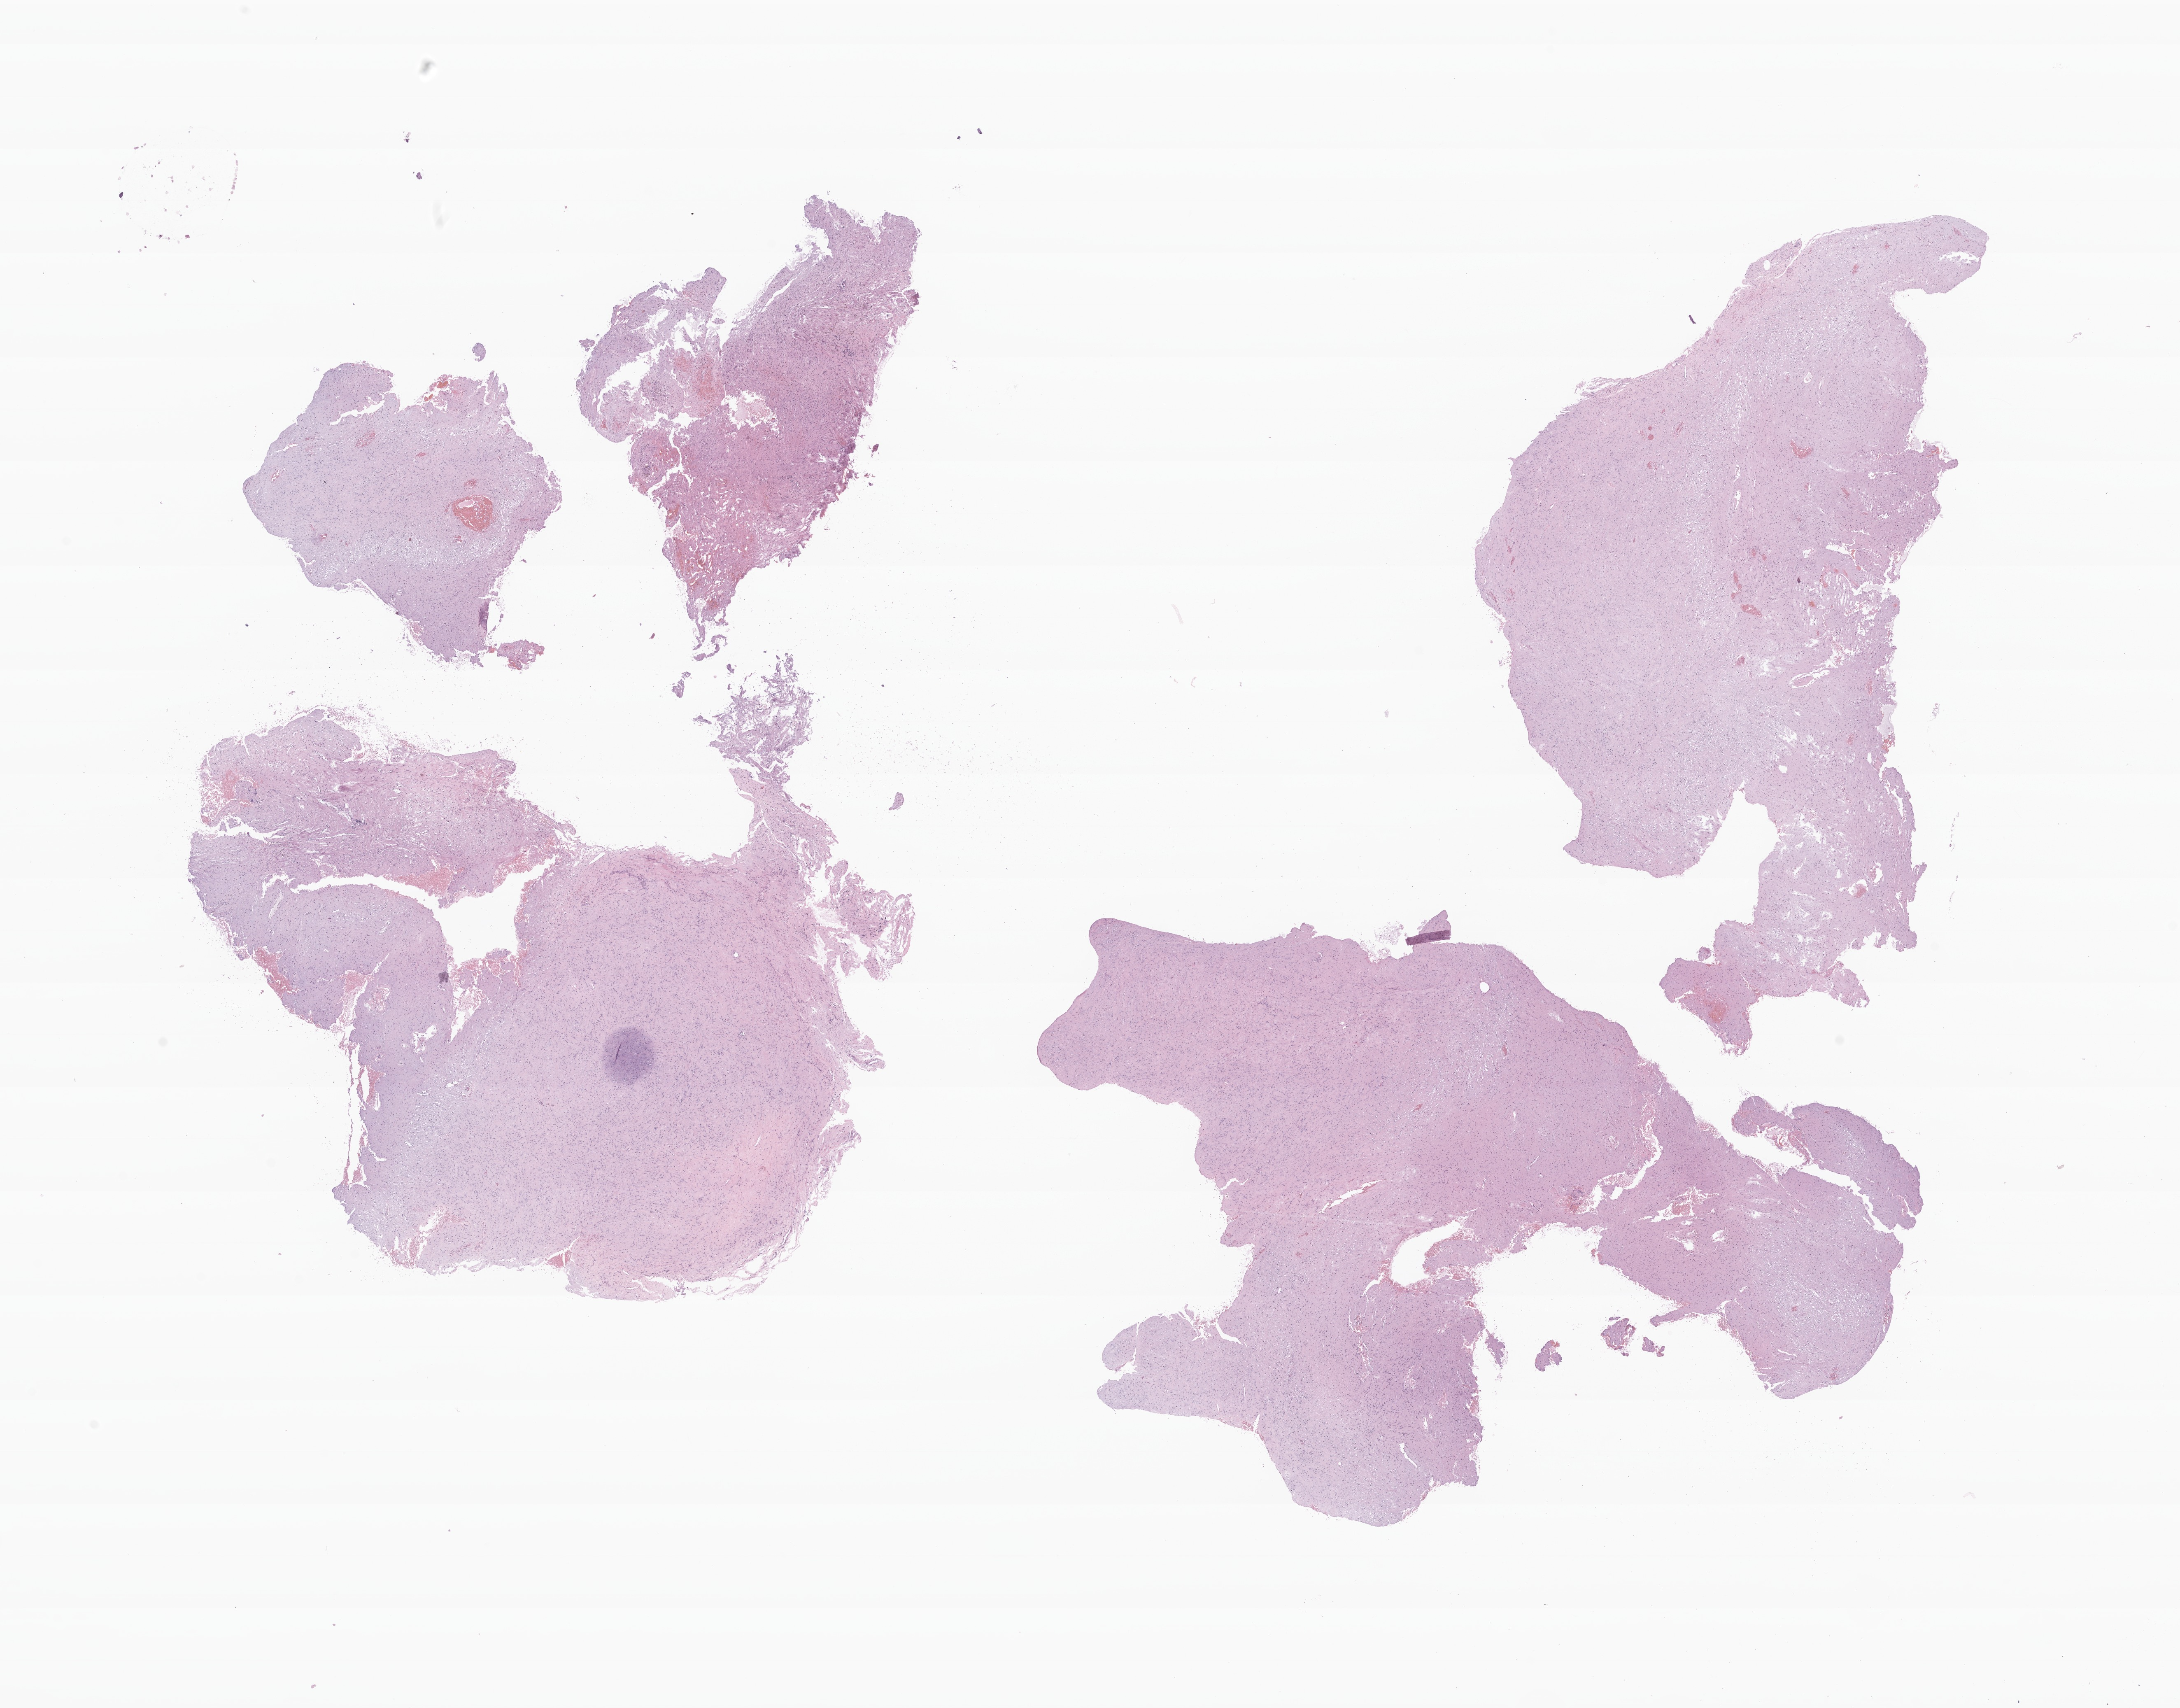
Digitized haematoxylin and eosin-stained section of tumor tissue from the brain, shown as a low-resolution overview of the whole scanned area (about 22.3 x 17.4 mm), formalin-fixed paraffin-embedded section. Male patient, age 185 months (15 years 5 months).
• diagnosis (ICD-O-3 morphology term): Neuroma, NOS